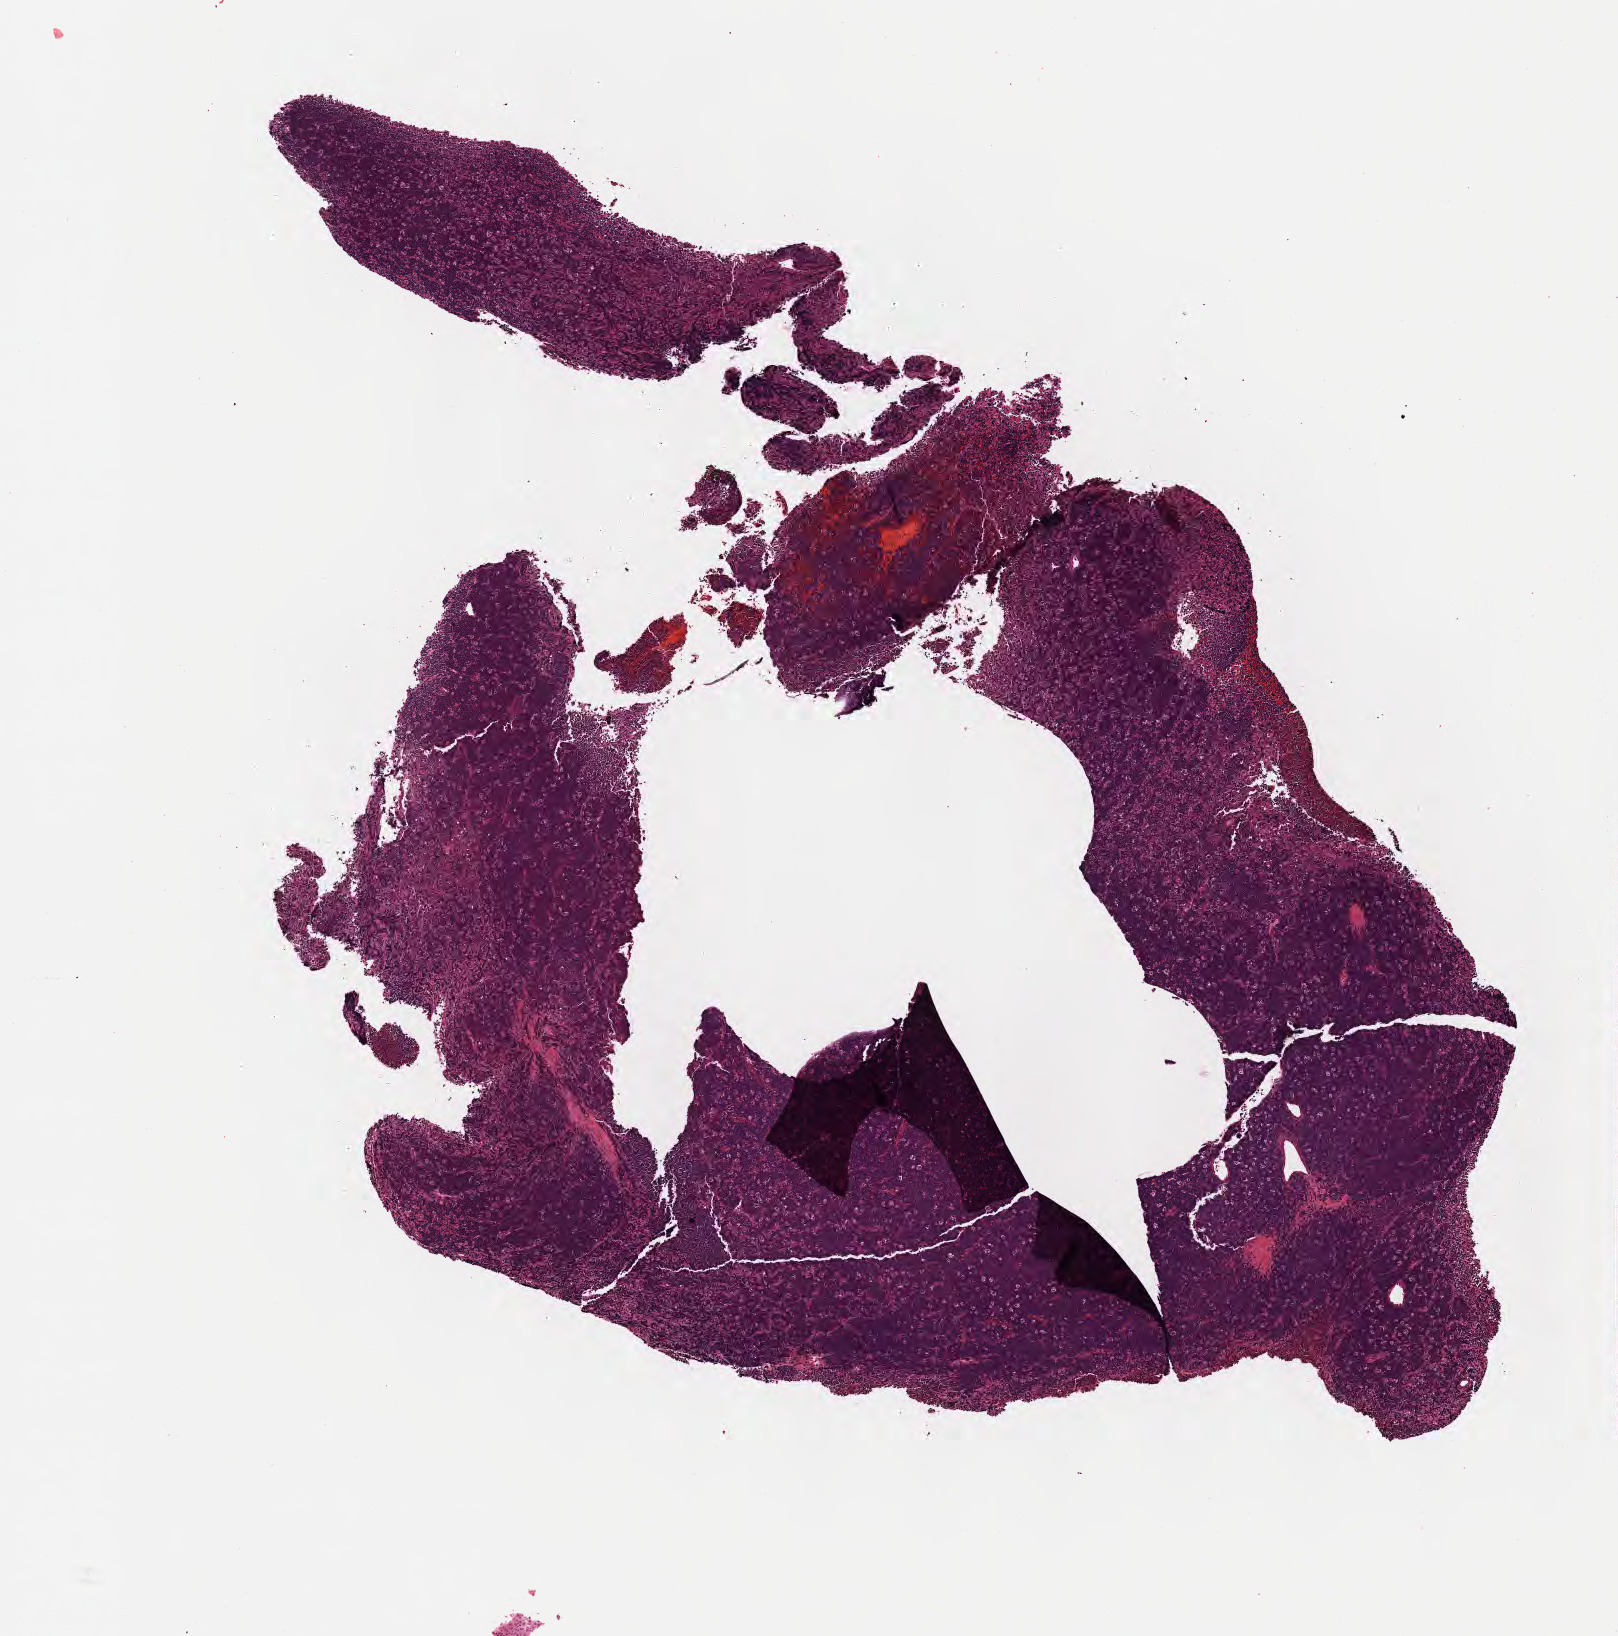
Digitized hematoxylin and eosin (H&E)-stained section — shown as a low-resolution overview of the whole scanned area (about 6.5 x 6.6 mm); formalin-fixed paraffin-embedded section; specimen: primary tumor; site: cranium. Male, age 6 years at initial diagnosis. Composition of this section per pathologist review: tumor cells 90%, tumor nuclei 95%, stromal cells 5%, necrosis 5%, normal cells 0%. Infiltration values recorded for this section: lymphocyte infiltration 40%, monocyte infiltration 30%, neutrophil infiltration 5%.
Ann Arbor stage (patient): Stage IV. Diagnosis: Burkitt lymphoma, NOS. Section: top of the tissue portion.